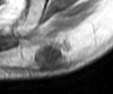
MRI of an extremity soft-tissue mass, one axial slice; position 14 of 42 along the scan axis; MR volume resampled by the dataset authors to the PET/CT grid (not the native acquisition matrix); 3.27 mm slice thickness; 113 × 94 image matrix, field of view 110 × 92 mm. Male patient. From the clinical record (not read from this slice): histological type: leiomyosarcoma; grade: intermediate; site of the primary tumour: left pelvis.
Annotated regions visible in this slice (expert contour drawn on MRI and transferred to this co-registered scan by the dataset authors):
- gross tumour volume (mass): bounding box <37,41,71,69> (left, top, right, bottom; pixels)